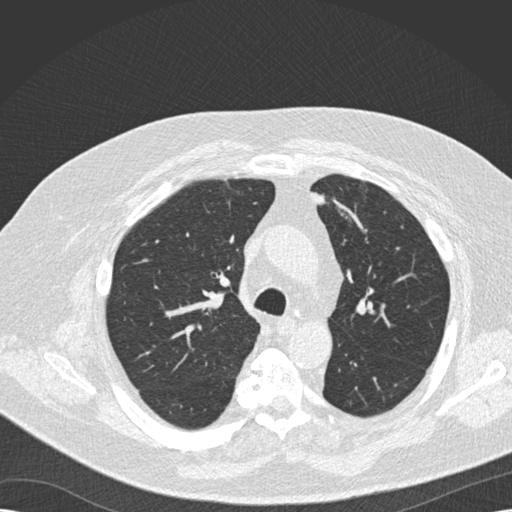
Low-dose screening chest CT, one axial slice. Position 116 of 173 along the scan axis. Reconstruction kernel B30f. Lung window (W 1500 / L -600 HU). 2 mm slice thickness. 512 × 512 image matrix, field of view 370 × 370 mm.
Structures marked on this image (outlined manually by an expert reader):
- lesion 1 (tumor, upper lobe of left lung): bounding box (x1, y1, x2, y2) in pixels: (312, 192, 325, 204)